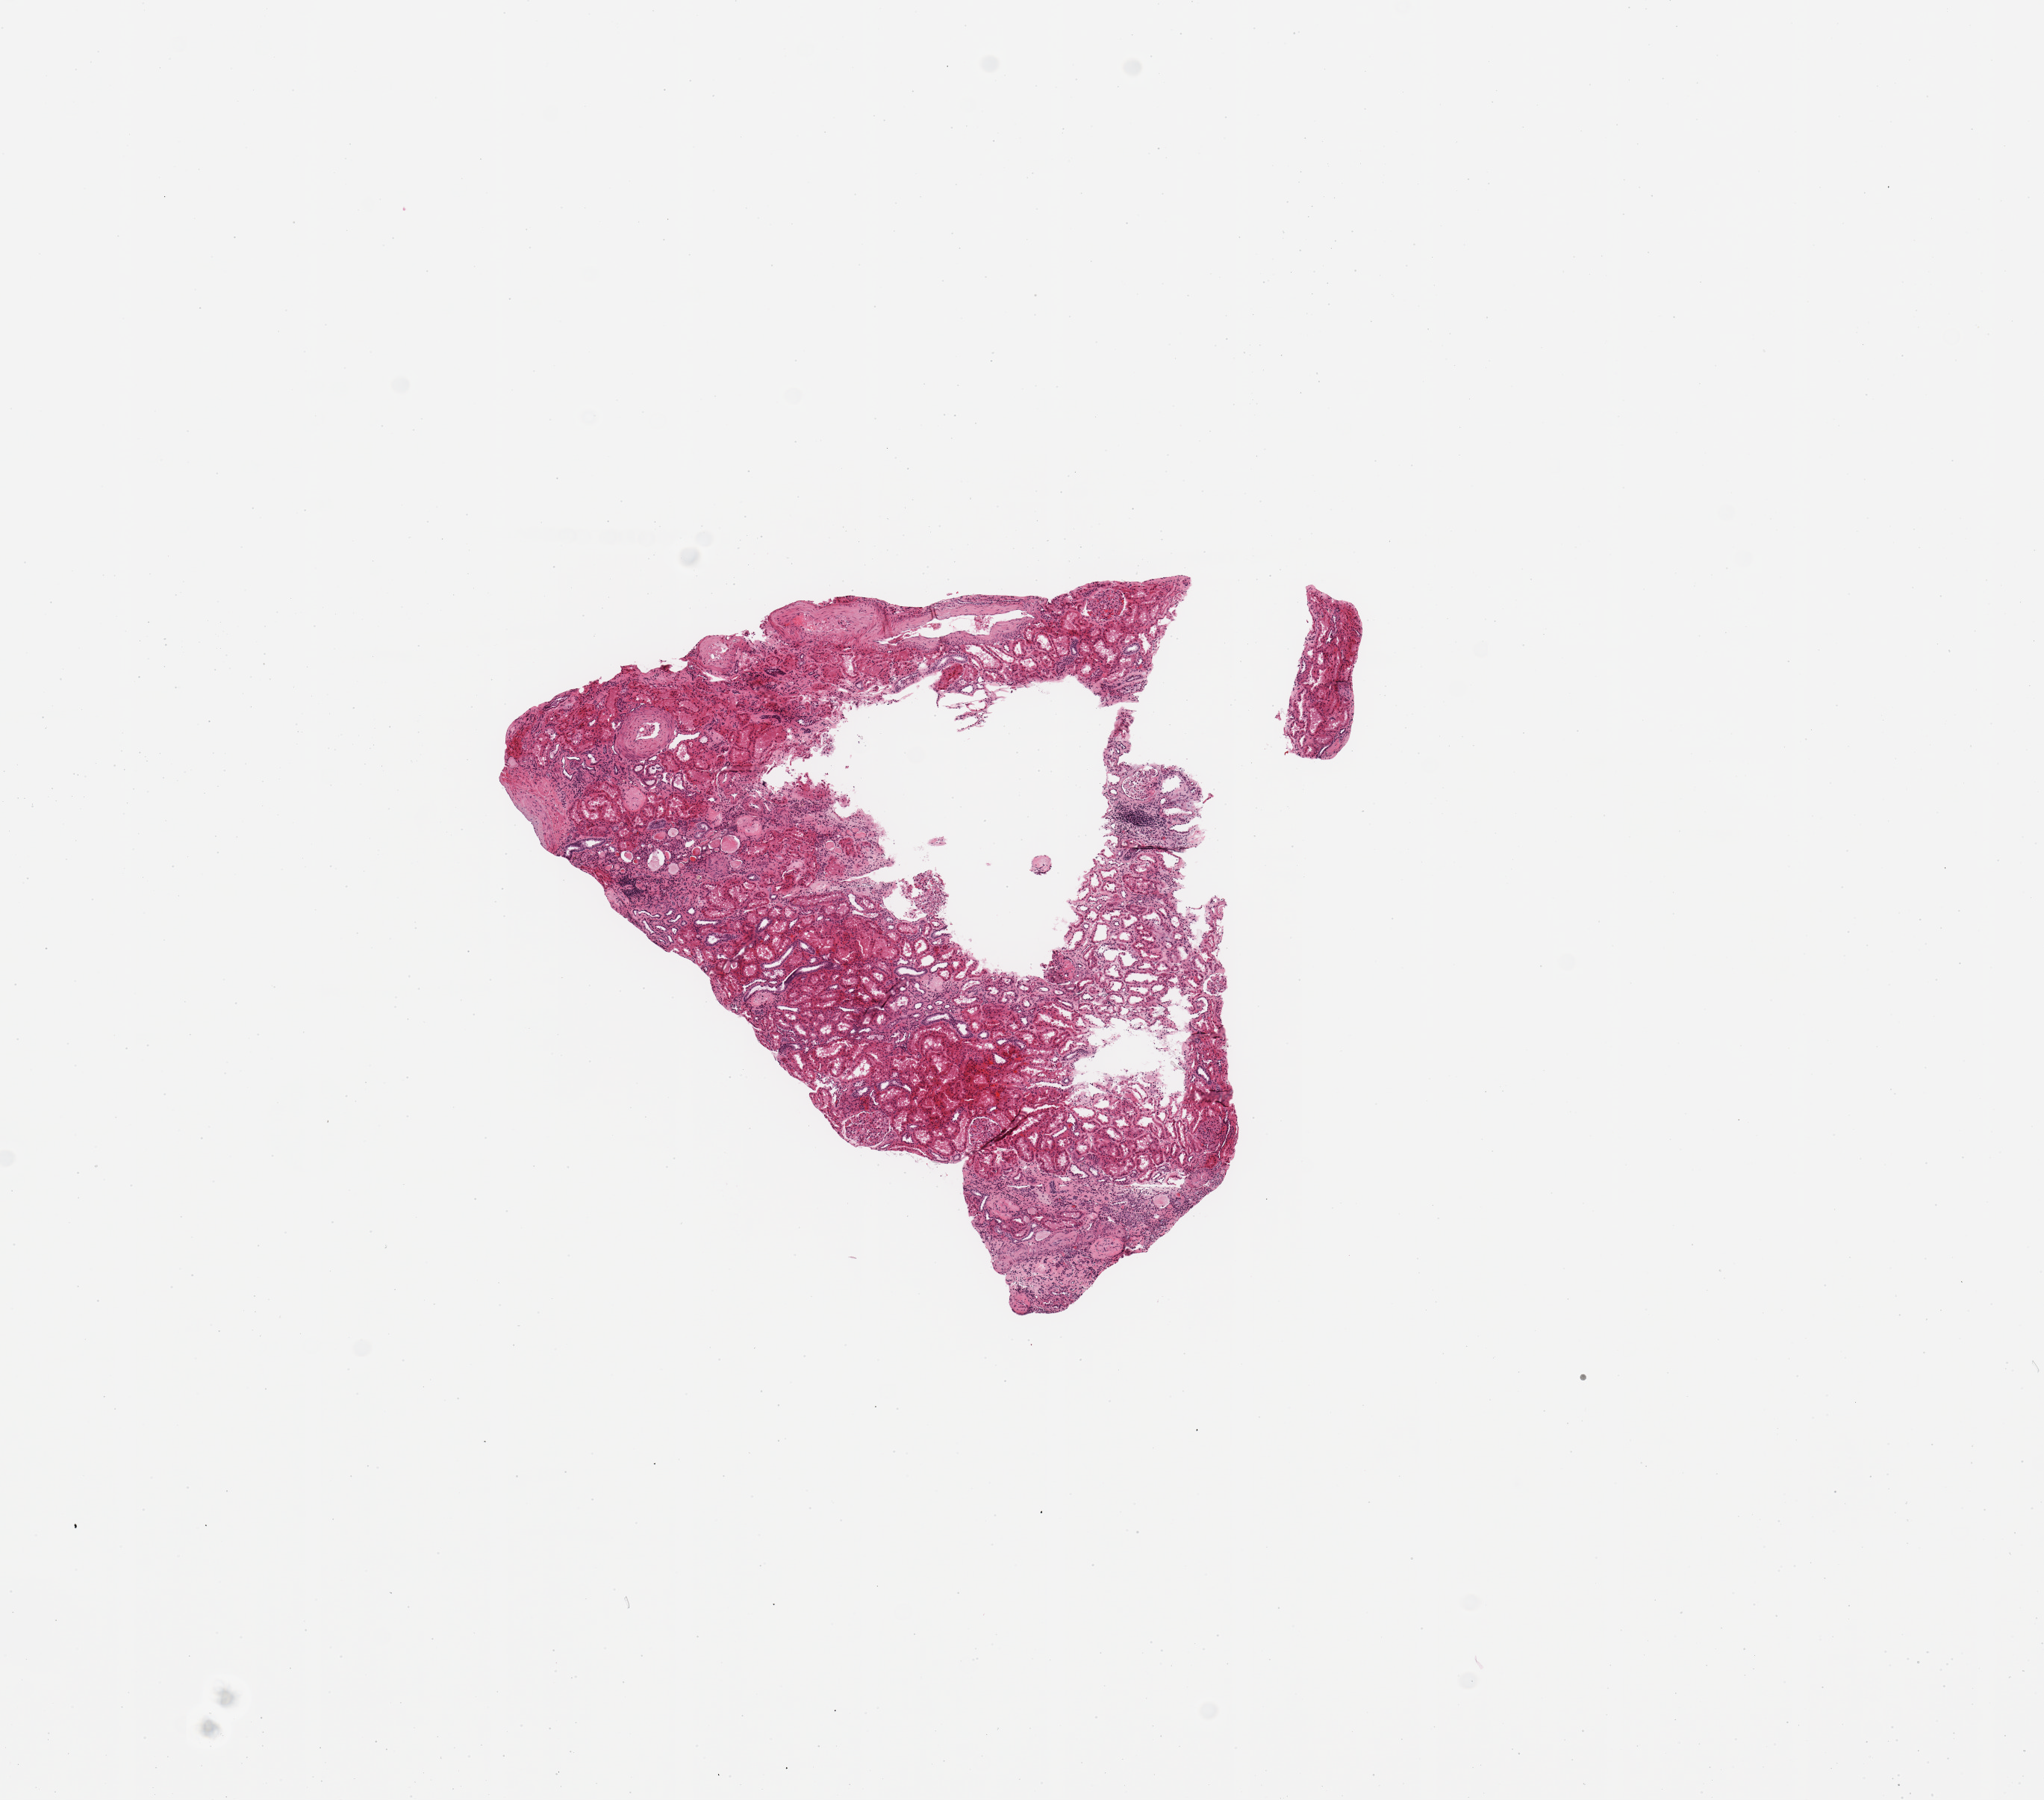
Digitized H&E tissue section (whole slide) — whole scanned area (about 10.8 x 9.5 mm) shown as a low-resolution overview, normal (non-tumour) tissue sample, sampled site: kidney. Male, 67 y/o.
• this section: normal (non-tumour) tissue from the same patient
• patient diagnosis: Renal cell carcinoma, NOS